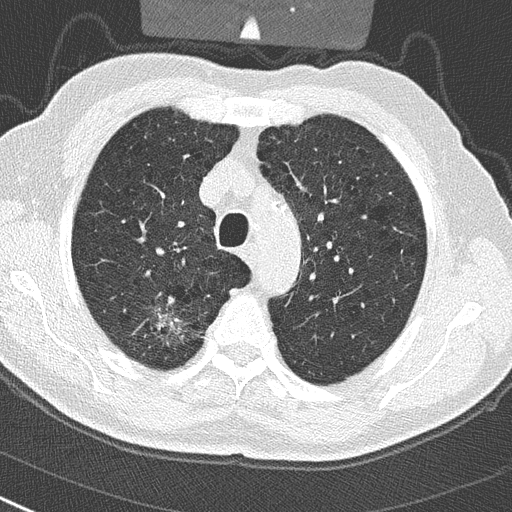
Low-dose screening chest CT, one axial slice. Position 221 of 290 along the scan axis. Reconstruction kernel B50f. Lung window (W 1500 / L -600 HU). 2 mm slice thickness. 512 × 512 image matrix, field of view 300 × 300 mm.
Outlined on this slice (outlined manually by an expert reader):
- lesion 1 (tumor, upper lobe of right lung): box from (x=155, y=313) to (x=188, y=349) px